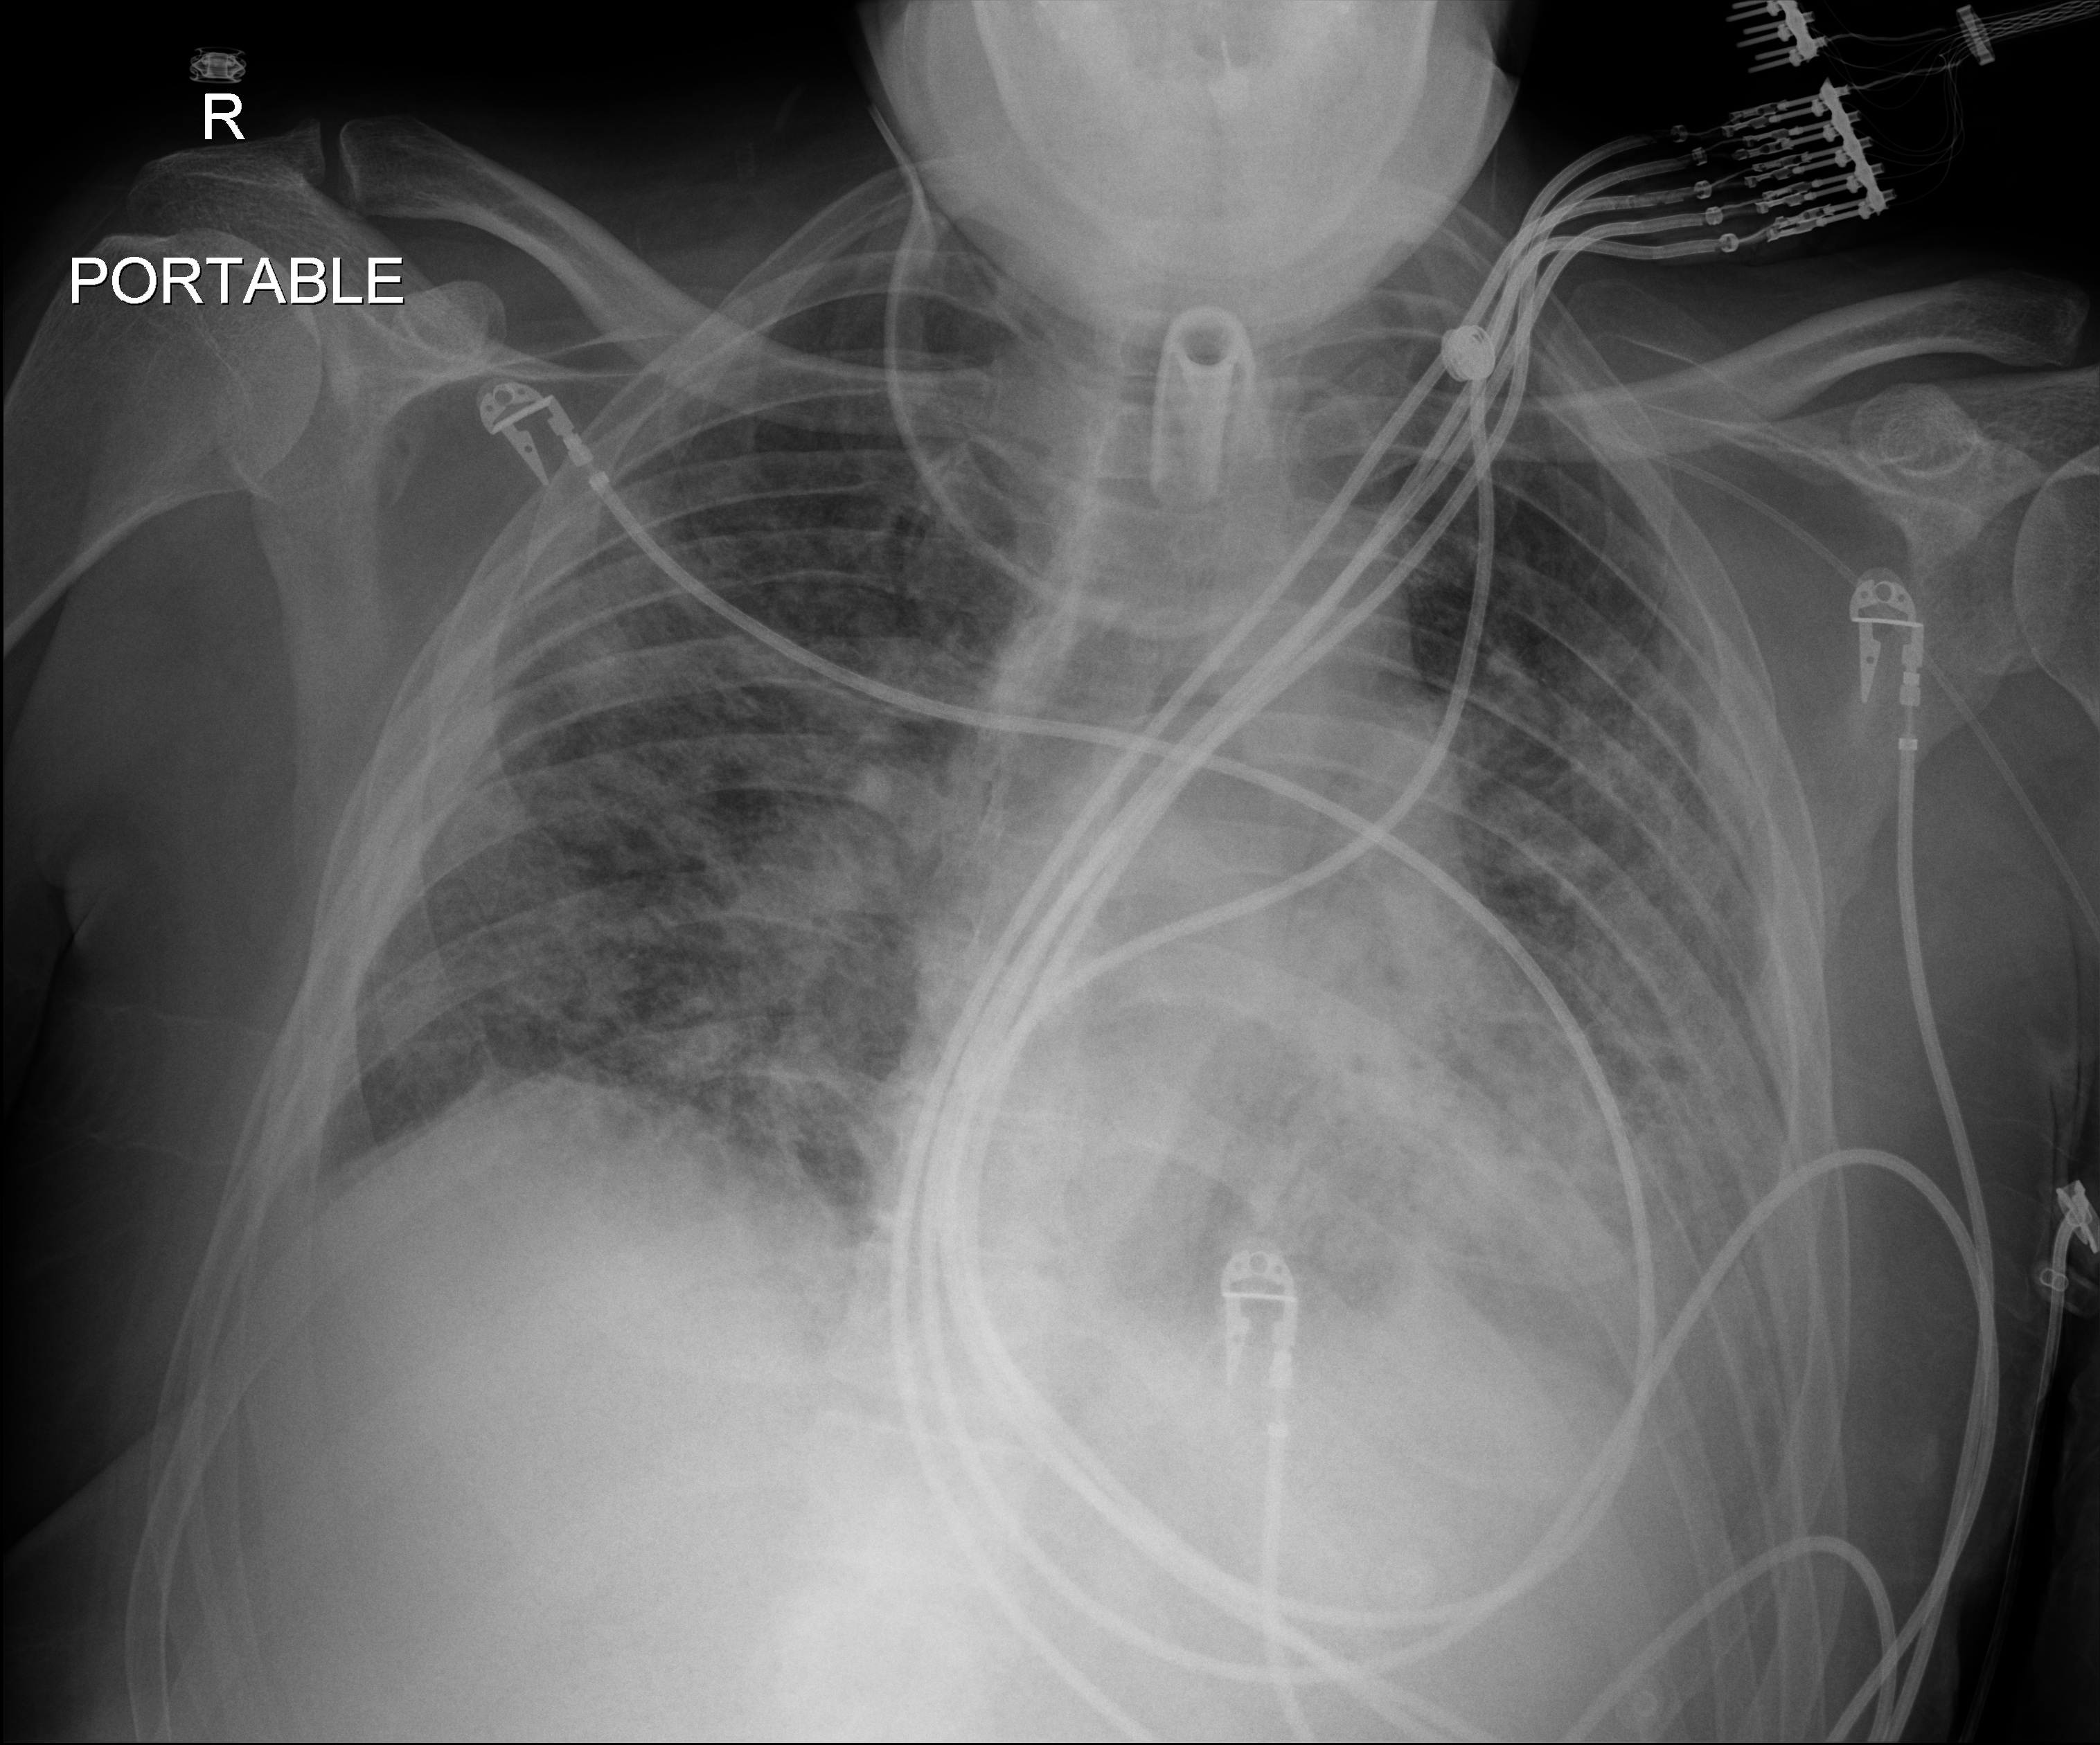
Chest X-ray (portable). Male patient hospitalised with COVID-19, age 18–59 years.
From the hospital-stay record, not from the radiograph (when in the stay this image was taken is not recorded): admitted to intensive care during this hospital stay: yes.